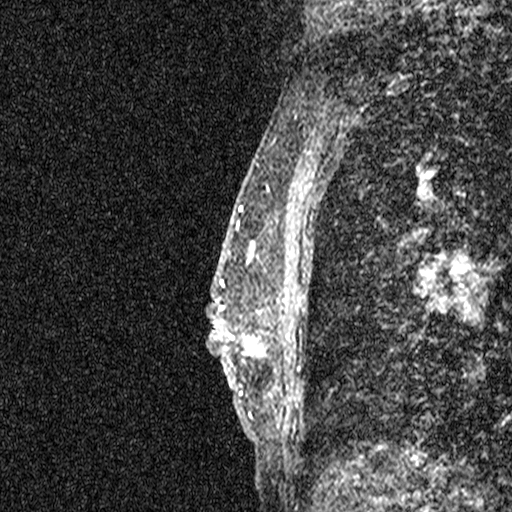
Breast MRI (dynamic contrast-enhanced), one sagittal slice. Position 21 of 44 along the scan axis. Dynamic contrast-enhanced study with each time point stored as its own series, time point 2 of 3 at this slice position (early post-contrast, ordered by acquisition time). 1.5 T. TE 4.5 ms, TR 11 ms. 2.05 mm slice thickness. 512 × 512 image matrix. Patient: female, 44 years. Case-level facts recorded for this patient, not image findings: setting: breast cancer imaged before/during neoadjuvant chemotherapy; receptor status: HR-positive, HER2-negative.
Annotated regions visible in this slice (semi-automatic segmentation, software-assisted and operator-edited):
- analysis volume of interest (the breast-tissue region the enhancement analysis was run in; not a lesion): bounding box (x1, y1, x2, y2) in pixels: (204, 254, 275, 401)
- tumour enhancement mask (voxels above the 90 % enhancement threshold inside the analysis volume of interest): (207, 254, 268, 400)